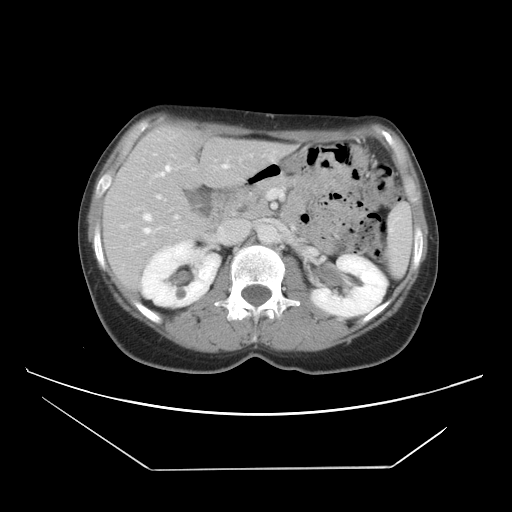
Contrast-enhanced abdominal CT, one axial slice; position 24 of 42 along the scan axis; 120 kVp; soft-tissue window (W 400 / L 40 HU); 5 mm slice thickness; 512 × 512 image matrix, field of view 399 × 399 mm. Female patient, age 52 years. From the clinical record (not read from this slice): diagnosis: colorectal cancer liver metastases, imaged before liver resection; multiple liver metastases: yes; largest metastasis: 5.5 cm; disease in both lobes: yes.
Annotated regions visible in this slice (expert manual segmentation):
- hepatic veins: bounding box <142,138,229,235> (left, top, right, bottom; pixels)
- liver: <105,127,288,286>
- planned liver remnant (the part of the liver to remain after resection): <113,127,218,207>
- portal vein (with intrahepatic branches): <156,156,270,219>